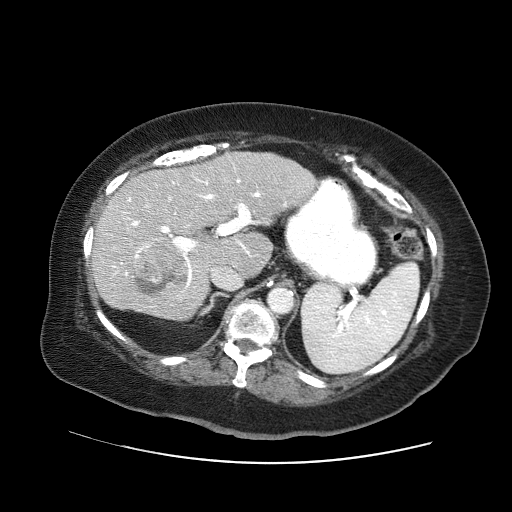
Contrast-enhanced abdominal CT (liver protocol), one axial slice; position 34 of 71 along the scan axis; reconstruction kernel STANDARD; 120 kVp; soft-tissue window (W 400 / L 40 HU); 2.5 mm slice thickness; 512 × 512 image matrix, field of view 400 × 400 mm. From the clinical record (not read from this slice): diagnosis: hepatocellular carcinoma (patient treated with transarterial chemoembolisation; whether this scan precedes or follows treatment is not stated here); TNM stage (as recorded): Stage-II; Child-Pugh class: A; tumour differentiation: poorly differentiated; tumour nodularity: multinodular.
Annotated regions visible in this slice (semi-automatically segmented with operator editing):
- liver parenchyma outside the tumour (the mass and vessels are separate outlines, so this box may not span the whole liver): box from (x=90, y=152) to (x=316, y=320) px
- mass: (x=134, y=242)–(x=189, y=296)
- liver vessels: (x=113, y=166)–(x=287, y=289)